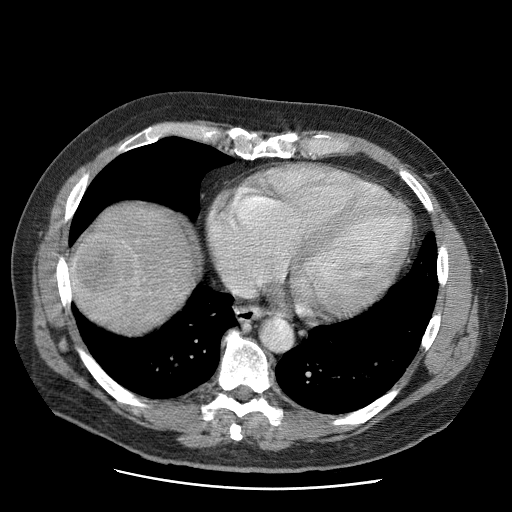
Contrast-enhanced abdominal CT (liver protocol), one axial slice; slice 61 of 81 in the series (ordered by position); 120 kVp; soft-tissue window (W 400 / L 40 HU); 512 × 512 image matrix, field of view 380 × 380 mm. Case-level facts recorded for this patient, not image findings: diagnosis: hepatocellular carcinoma (patient treated with transarterial chemoembolisation; whether this scan precedes or follows treatment is not stated here); TNM stage (as recorded): Stage-IIIA; Child-Pugh class: A; tumour size: 5.5 cm.
Outlined on this slice (semi-automatic segmentation, software-assisted and operator-edited):
- liver parenchyma outside the tumour (the mass and vessels are separate outlines, so this box may not span the whole liver): box from (x=68, y=204) to (x=200, y=330) px
- mass: (x=72, y=230)–(x=141, y=321)